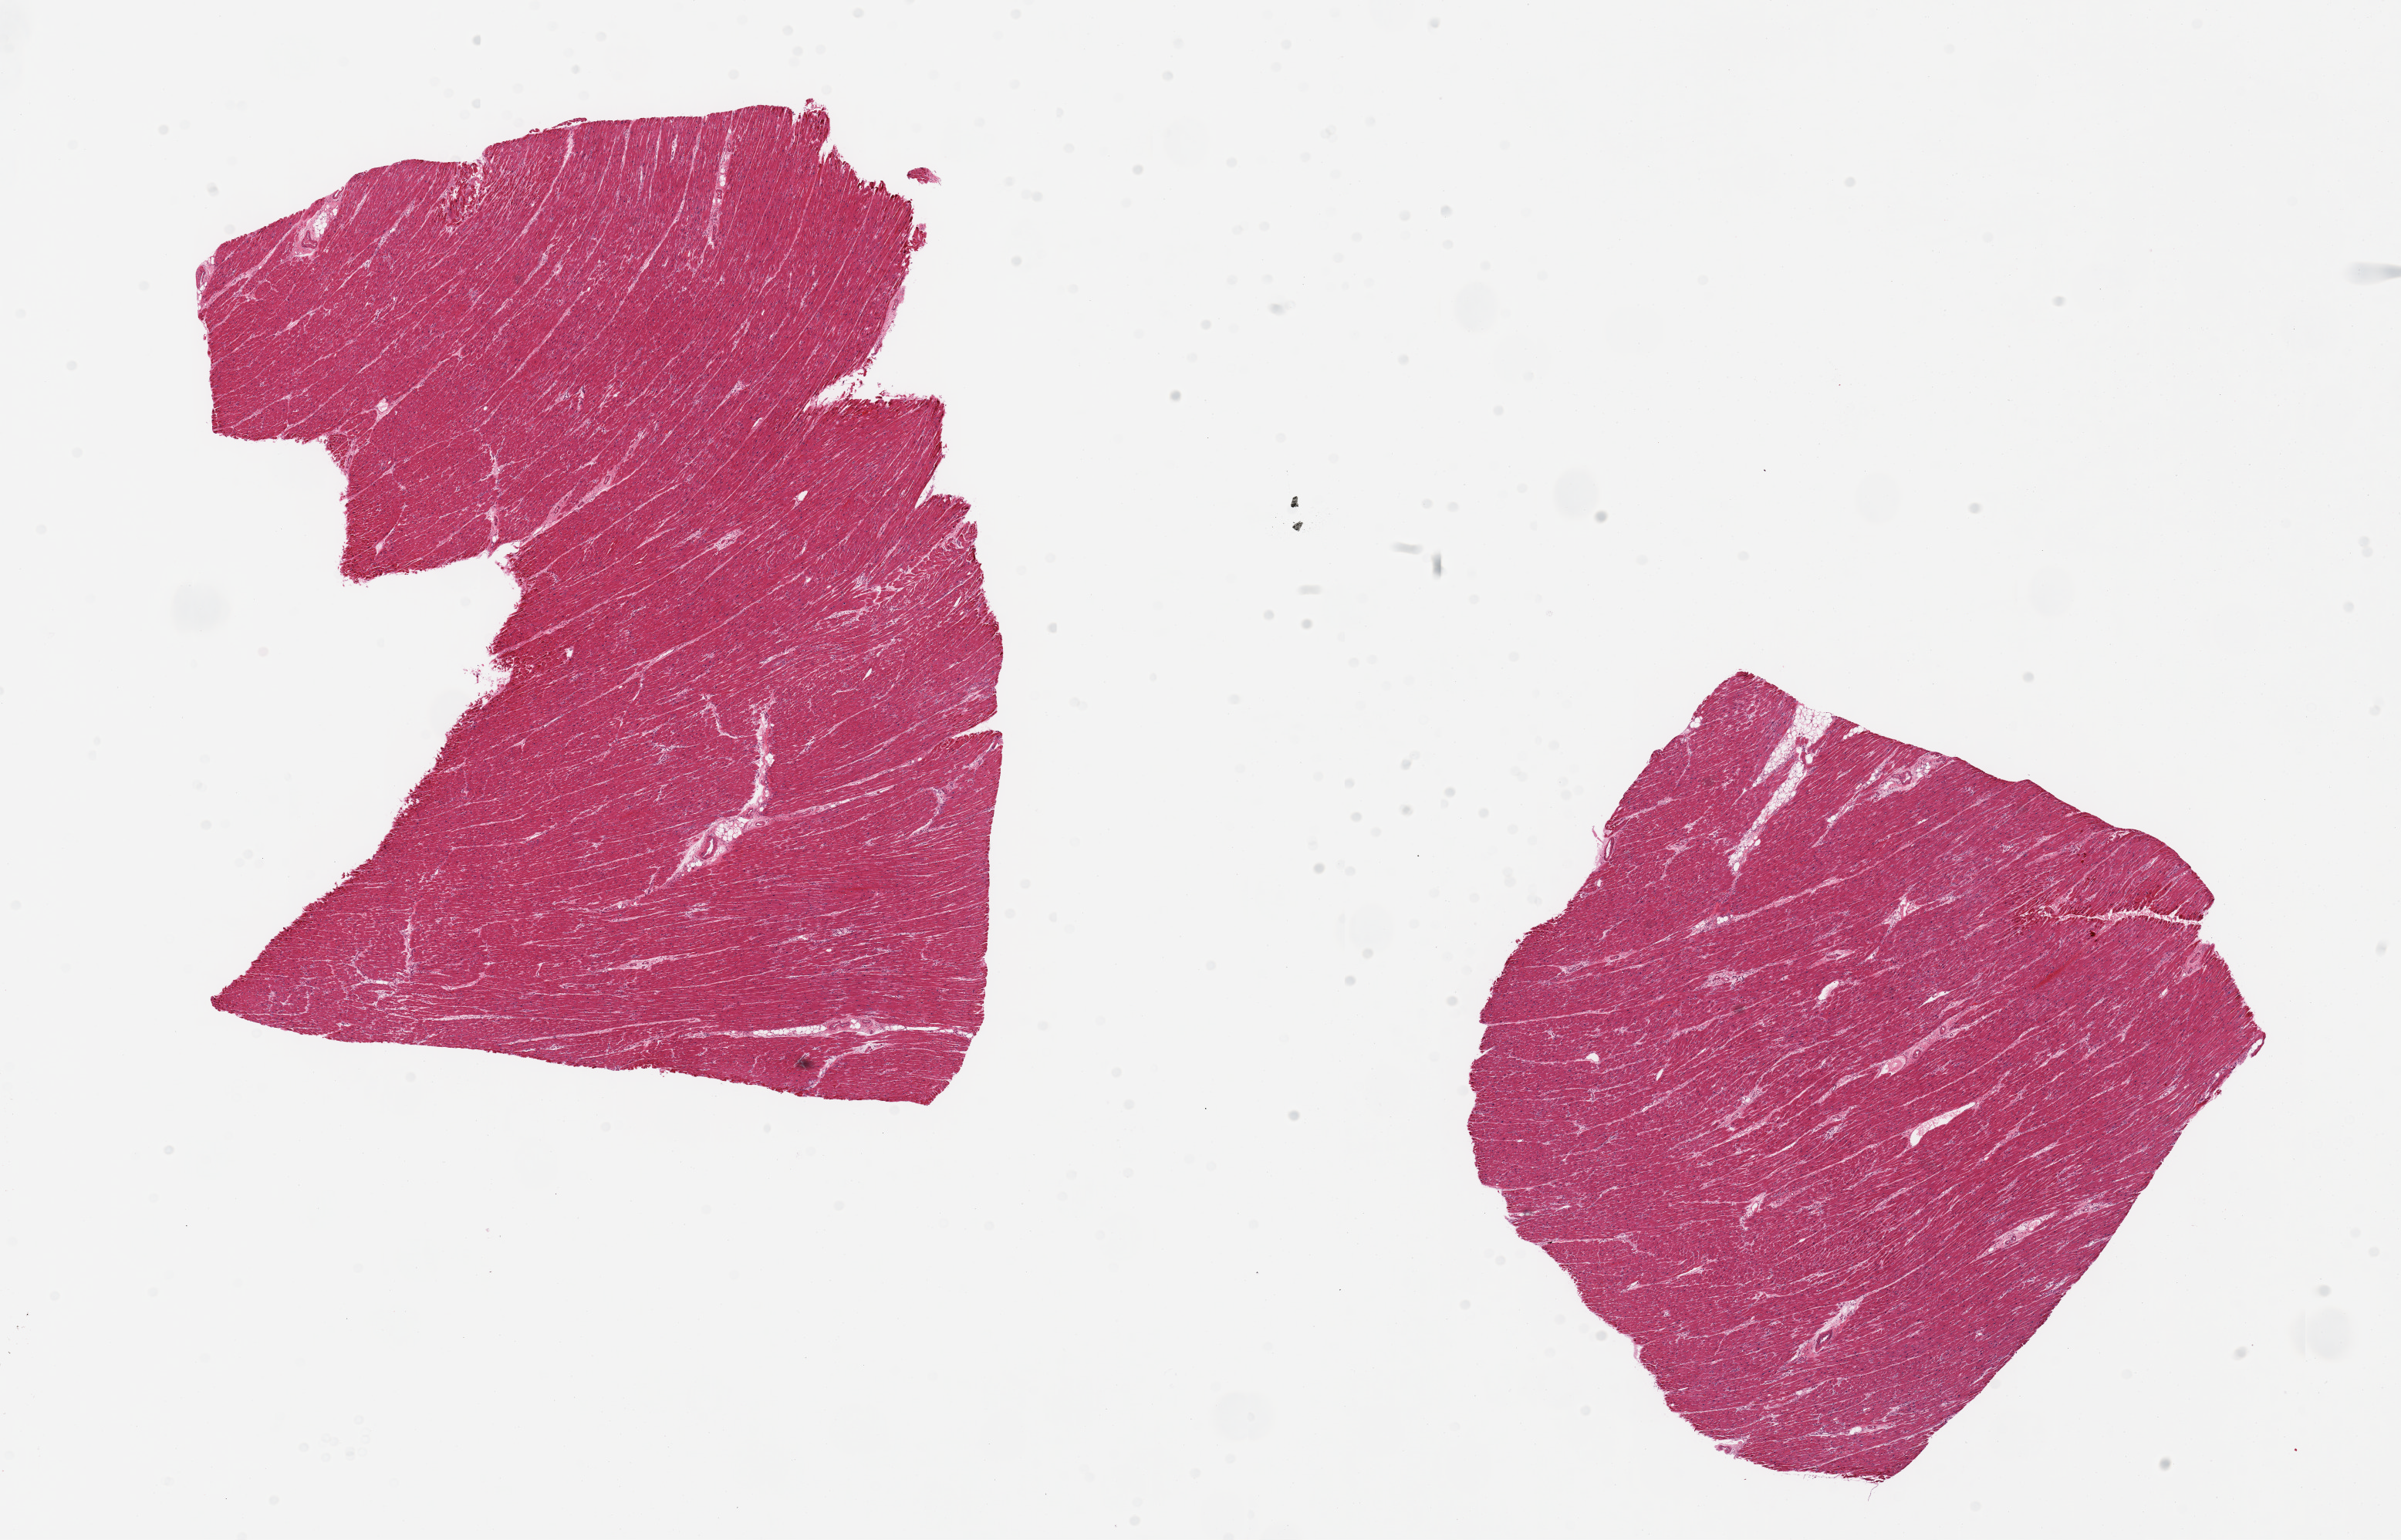
Whole-slide image, hematoxylin and eosin (H&E) stain, low-resolution overview of the scanned area, about 24.6 x 15.8 mm (acquisition: 20x scan), PAXgene-fixed paraffin-embedded (PFPE) section, section of heart (target tissue), donor tissue sample. Female donor.
Pathologist's review note for this sample: 2 pieces.